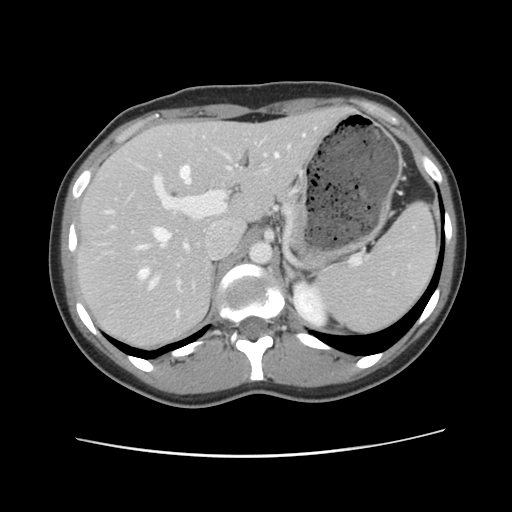
Contrast-enhanced abdominal CT, one axial slice; slice 74 of 134 in the series (ordered by position); 120 kVp; intravenous contrast given; soft-tissue window (W 400 / L 40 HU); 2.5 mm slice thickness; 512 × 512 image matrix, field of view 339 × 339 mm. Female patient, age 33 years. From the clinical record (not read from this slice): diagnosis: colorectal cancer liver metastases, imaged before liver resection; multiple liver metastases: yes; largest metastasis: 4.5 cm; disease in both lobes: yes.
Annotated regions visible in this slice (expert manual segmentation):
- hepatic veins: bounding box [x1, y1, x2, y2] px = [109, 153, 279, 317]
- liver: [78, 108, 347, 351]
- planned liver remnant (the part of the liver to remain after resection): [78, 109, 348, 350]
- portal vein (with intrahepatic branches): [150, 143, 293, 284]